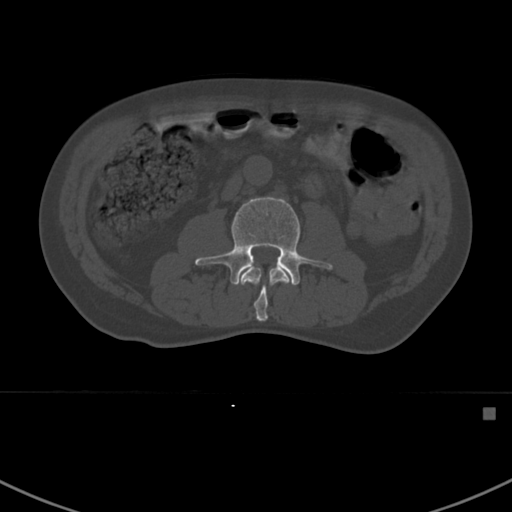
CT including the spine, one axial slice. Position 271 of 412 along the scan axis. Reconstruction kernel Br40s. Bone window (W 1800 / L 400 HU). 512 × 512 image matrix, field of view 358 × 358 mm. Patient: male, 59 years. From the clinical record (not read from this slice): primary cancer: prostate.
Annotated regions visible in this slice (semi-automatic segmentation, software-assisted and operator-edited):
- L2 vertebra: bounding box (x1, y1, x2, y2) in pixels: (240, 266, 290, 322)
- L3 vertebra: (195, 196, 333, 285)